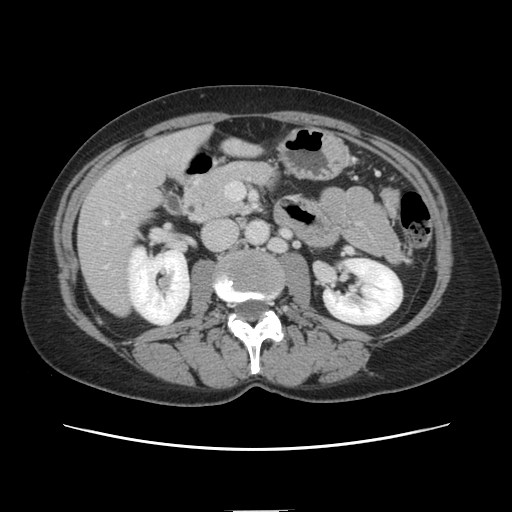
Contrast-enhanced abdominal CT, one axial slice; position 48 of 141 along the scan axis; 120 kVp; intravenous contrast given; soft-tissue window (W 400 / L 40 HU); 2.5 mm slice thickness; 512 × 512 image matrix. Female patient, age 63 years. From the clinical record (not read from this slice): diagnosis: colorectal cancer liver metastases, imaged before liver resection; multiple liver metastases: yes; largest metastasis: 3.2 cm; disease in both lobes: yes.
Outlined on this slice (manually delineated by an expert):
- liver: box from (x=79, y=129) to (x=253, y=314) px
- planned liver remnant (the part of the liver to remain after resection): (x=180, y=128)–(x=253, y=164)